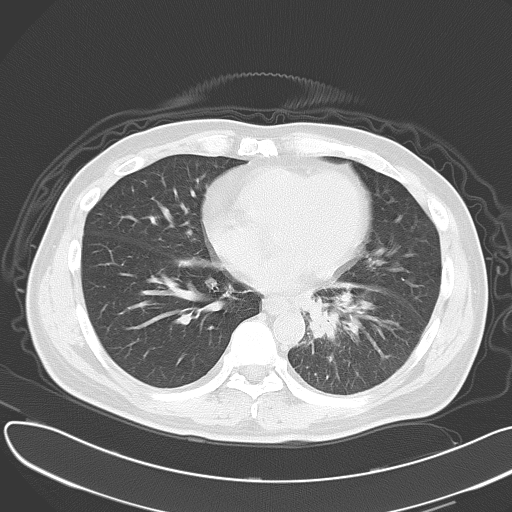
Chest CT, one axial slice; slice 21 of 55 in the series (ordered by position); 120 kVp; lung window (W 1500 / L -600 HU); 5 mm slice thickness; 512 × 512 image matrix, field of view 376 × 376 mm. Patient: male, 55 years. Case-level facts recorded for this patient, not image findings: clinical TNM (as recorded): T2 N3 M0; histopathological grade: G3.
Annotated regions visible in this slice (rectangle marked by the reading radiologist):
- lung tumour (recorded histology: small cell carcinoma): bounding box [x1, y1, x2, y2] px = [304, 300, 358, 362]